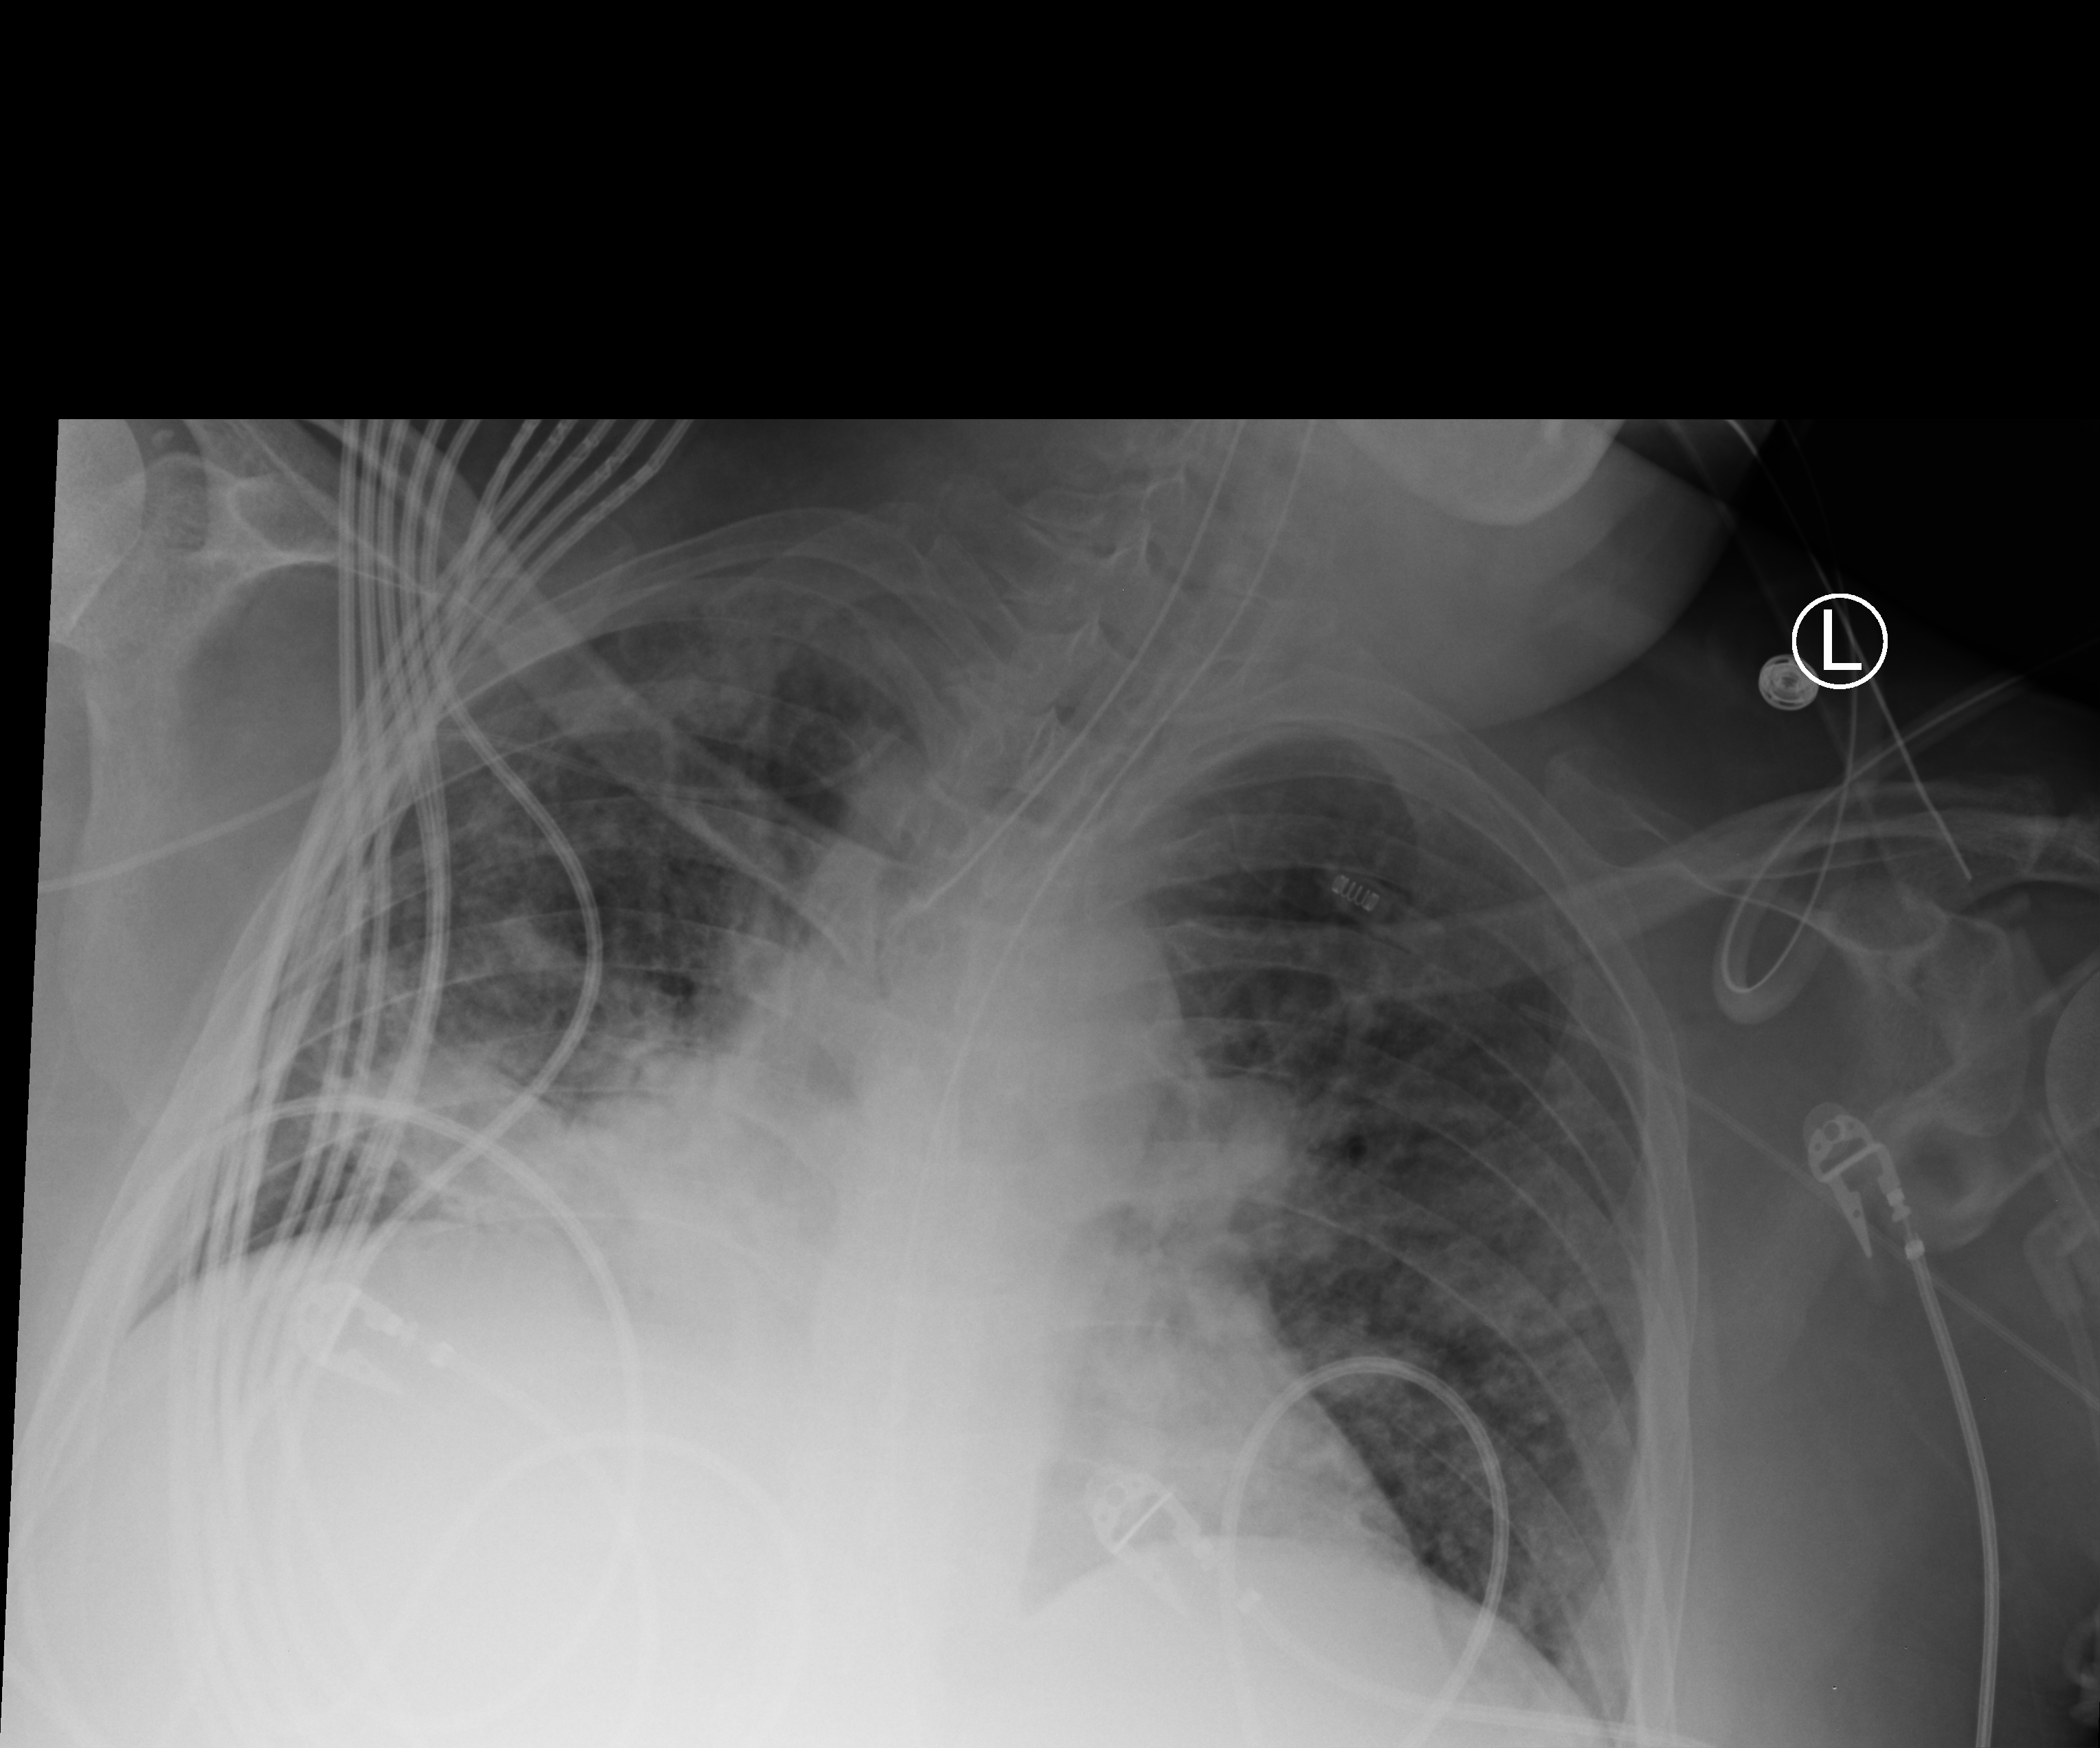
Bedside chest radiograph (computed radiography), anteroposterior (AP) projection. Adult patient hospitalised with COVID-19, age 18–59 years.
From the hospital-stay record, not from the radiograph (when in the stay this image was taken is not recorded): mechanically ventilated during this hospital stay: yes; COPD (admission record): no.